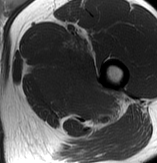
MRI of an extremity soft-tissue mass, one axial slice; position 64 of 70 along the scan axis; MR volume resampled by the dataset authors to the PET/CT grid (not the native acquisition matrix); 157 × 163 image matrix, field of view 153 × 159 mm. Male patient. Case-level facts recorded for this patient, not image findings: histological type: extraskeletal osteosarcoma; grade: high; site of the primary tumour: left adductur.
Outlined on this slice (expert contour drawn on MRI and transferred to this co-registered scan by the dataset authors):
- gross tumour volume (mass): box from (x=29, y=31) to (x=128, y=125) px